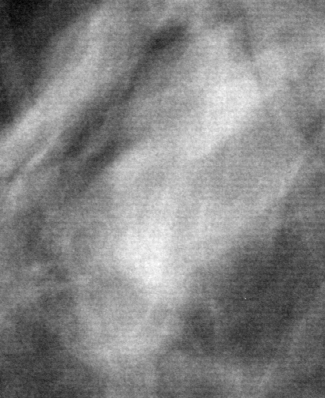
Cropped region of a digitized screen-film mammogram centred on a radiologist-marked abnormality, right breast, CC view, BI-RADS breast density category 1 (scale 1–4).
- Finding: mass, shape oval, margins circumscribed; BI-RADS assessment category 4; subtlety rating 5 on a 1 (subtle) to 5 (obvious) scale; pathology (as recorded): benign.